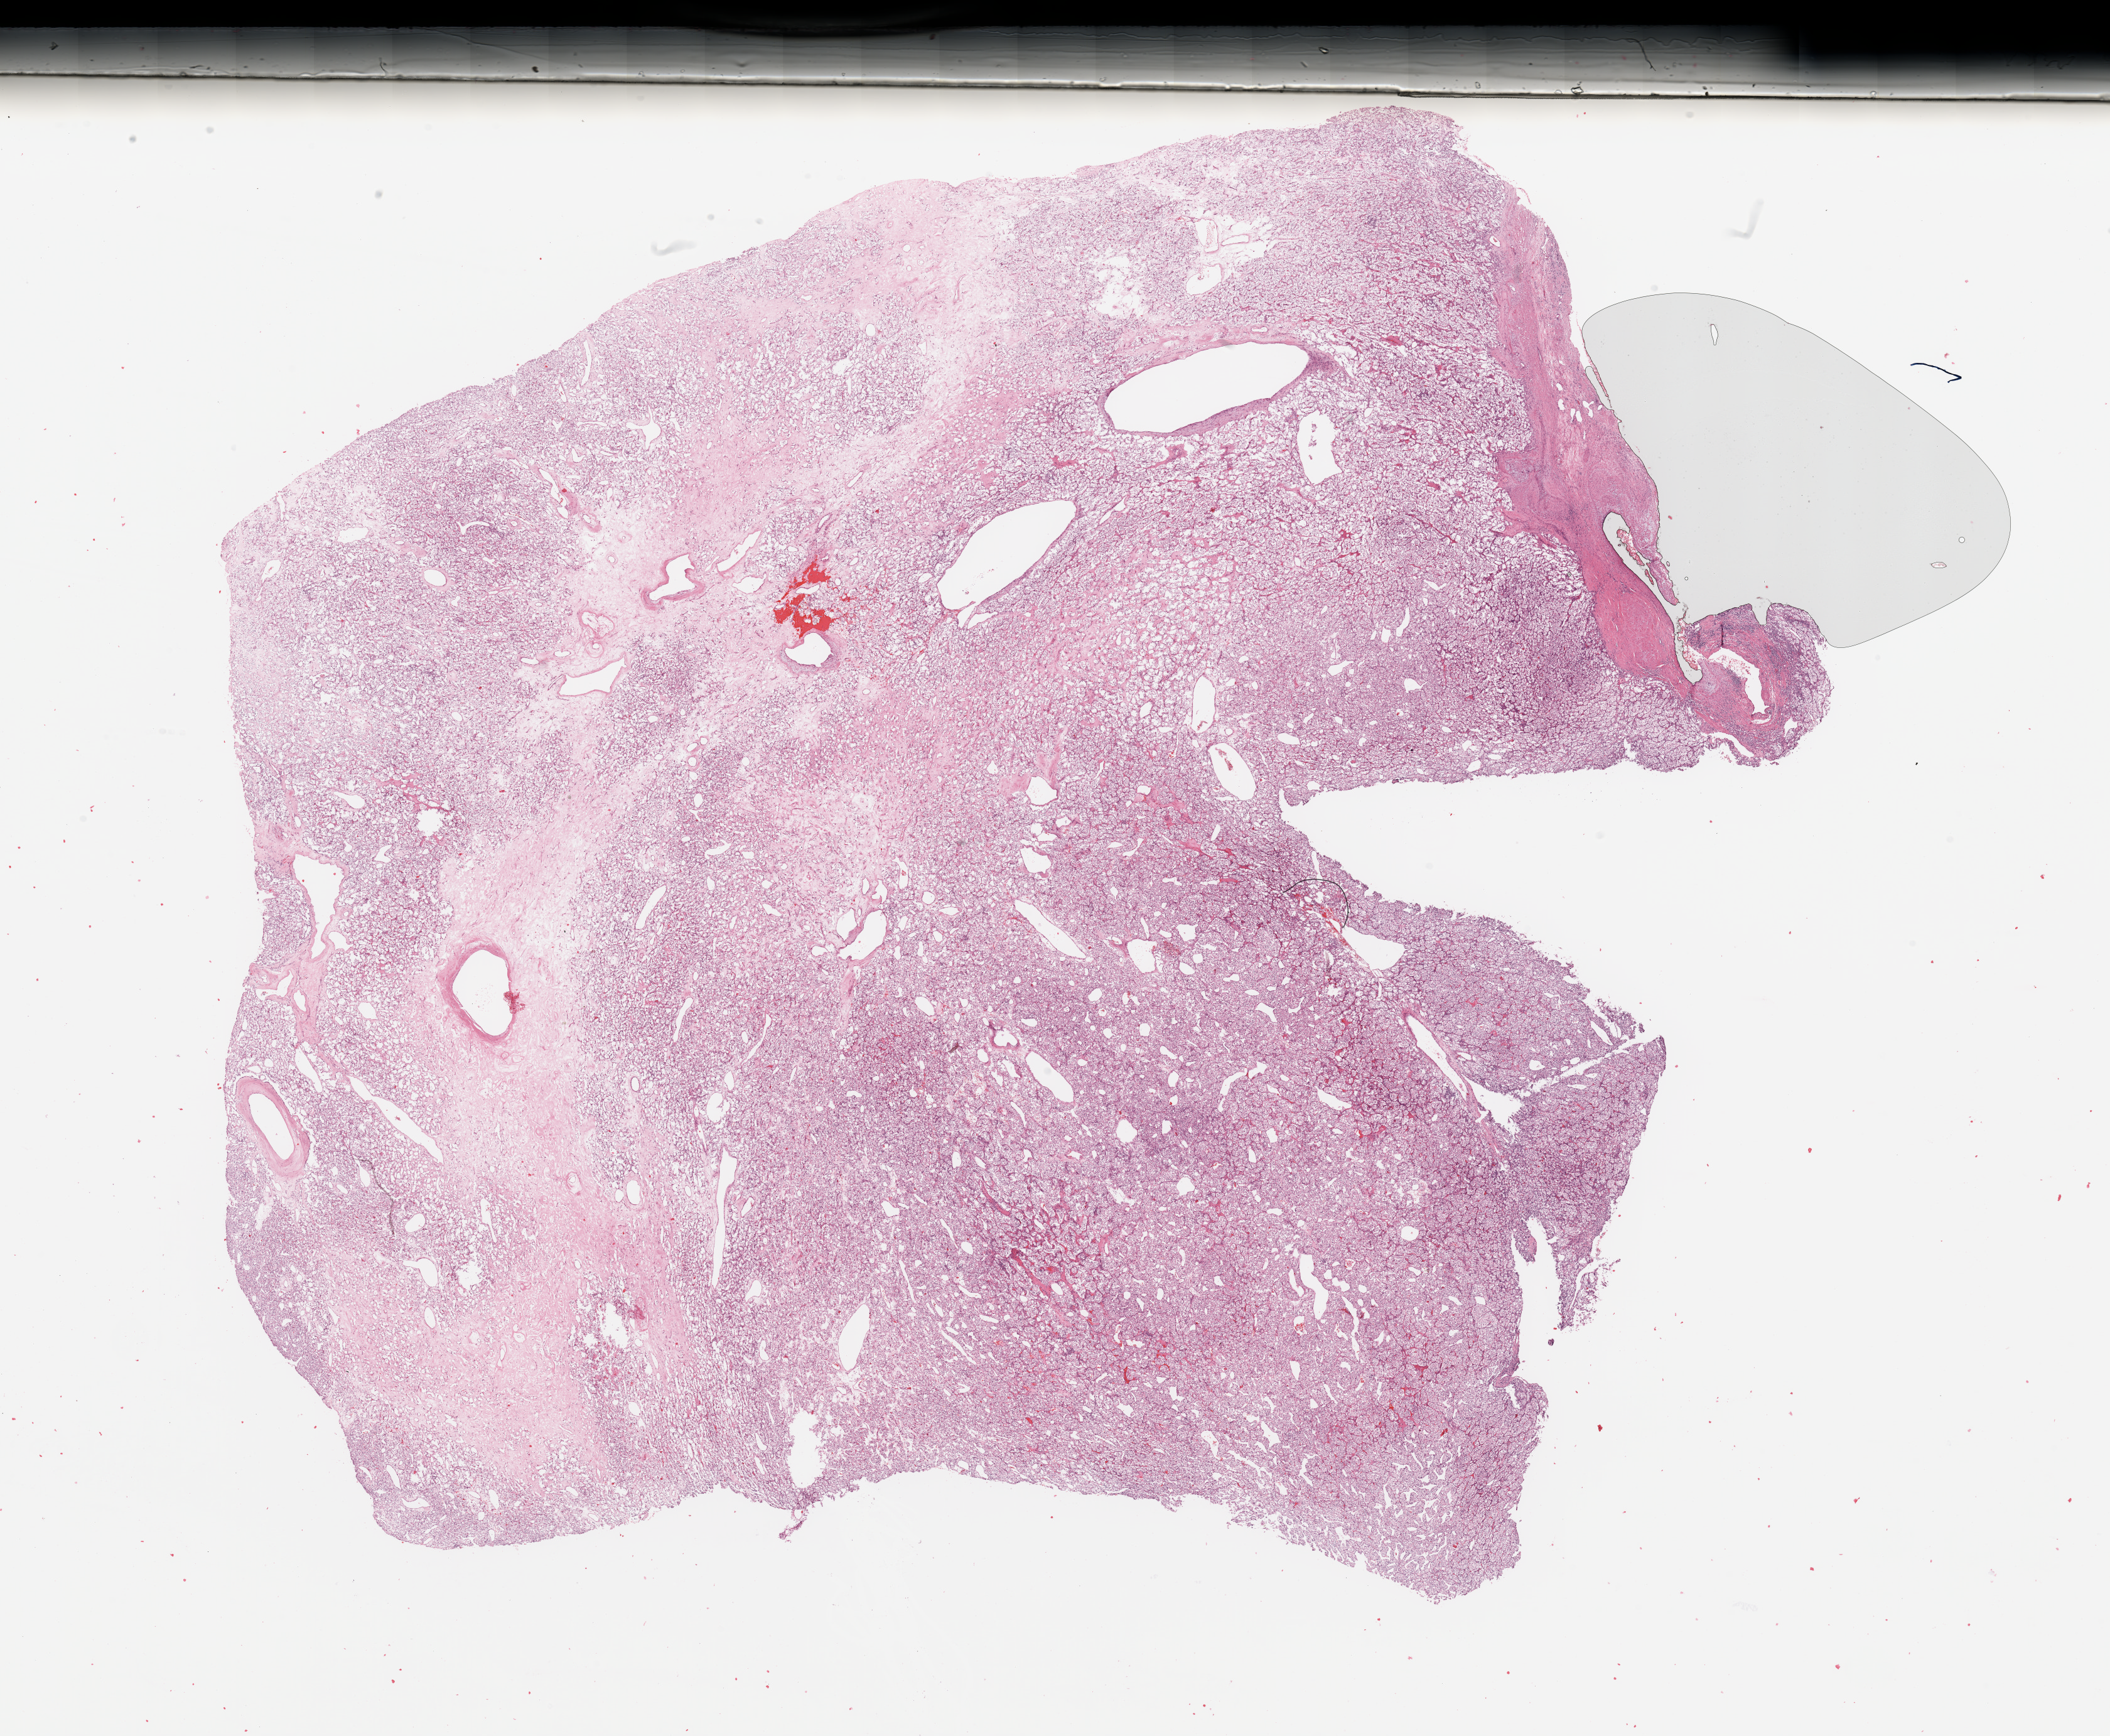
Whole-slide histology image, H&E — shown as a low-resolution overview of the whole scanned area (about 26.6 x 21.9 mm, slide scanned at 20x). Kidney, tumour tissue. Patient: female, age 69 years. Histologic grade: G2 (moderately differentiated).
Histologic diagnosis: Renal cell carcinoma, NOS.